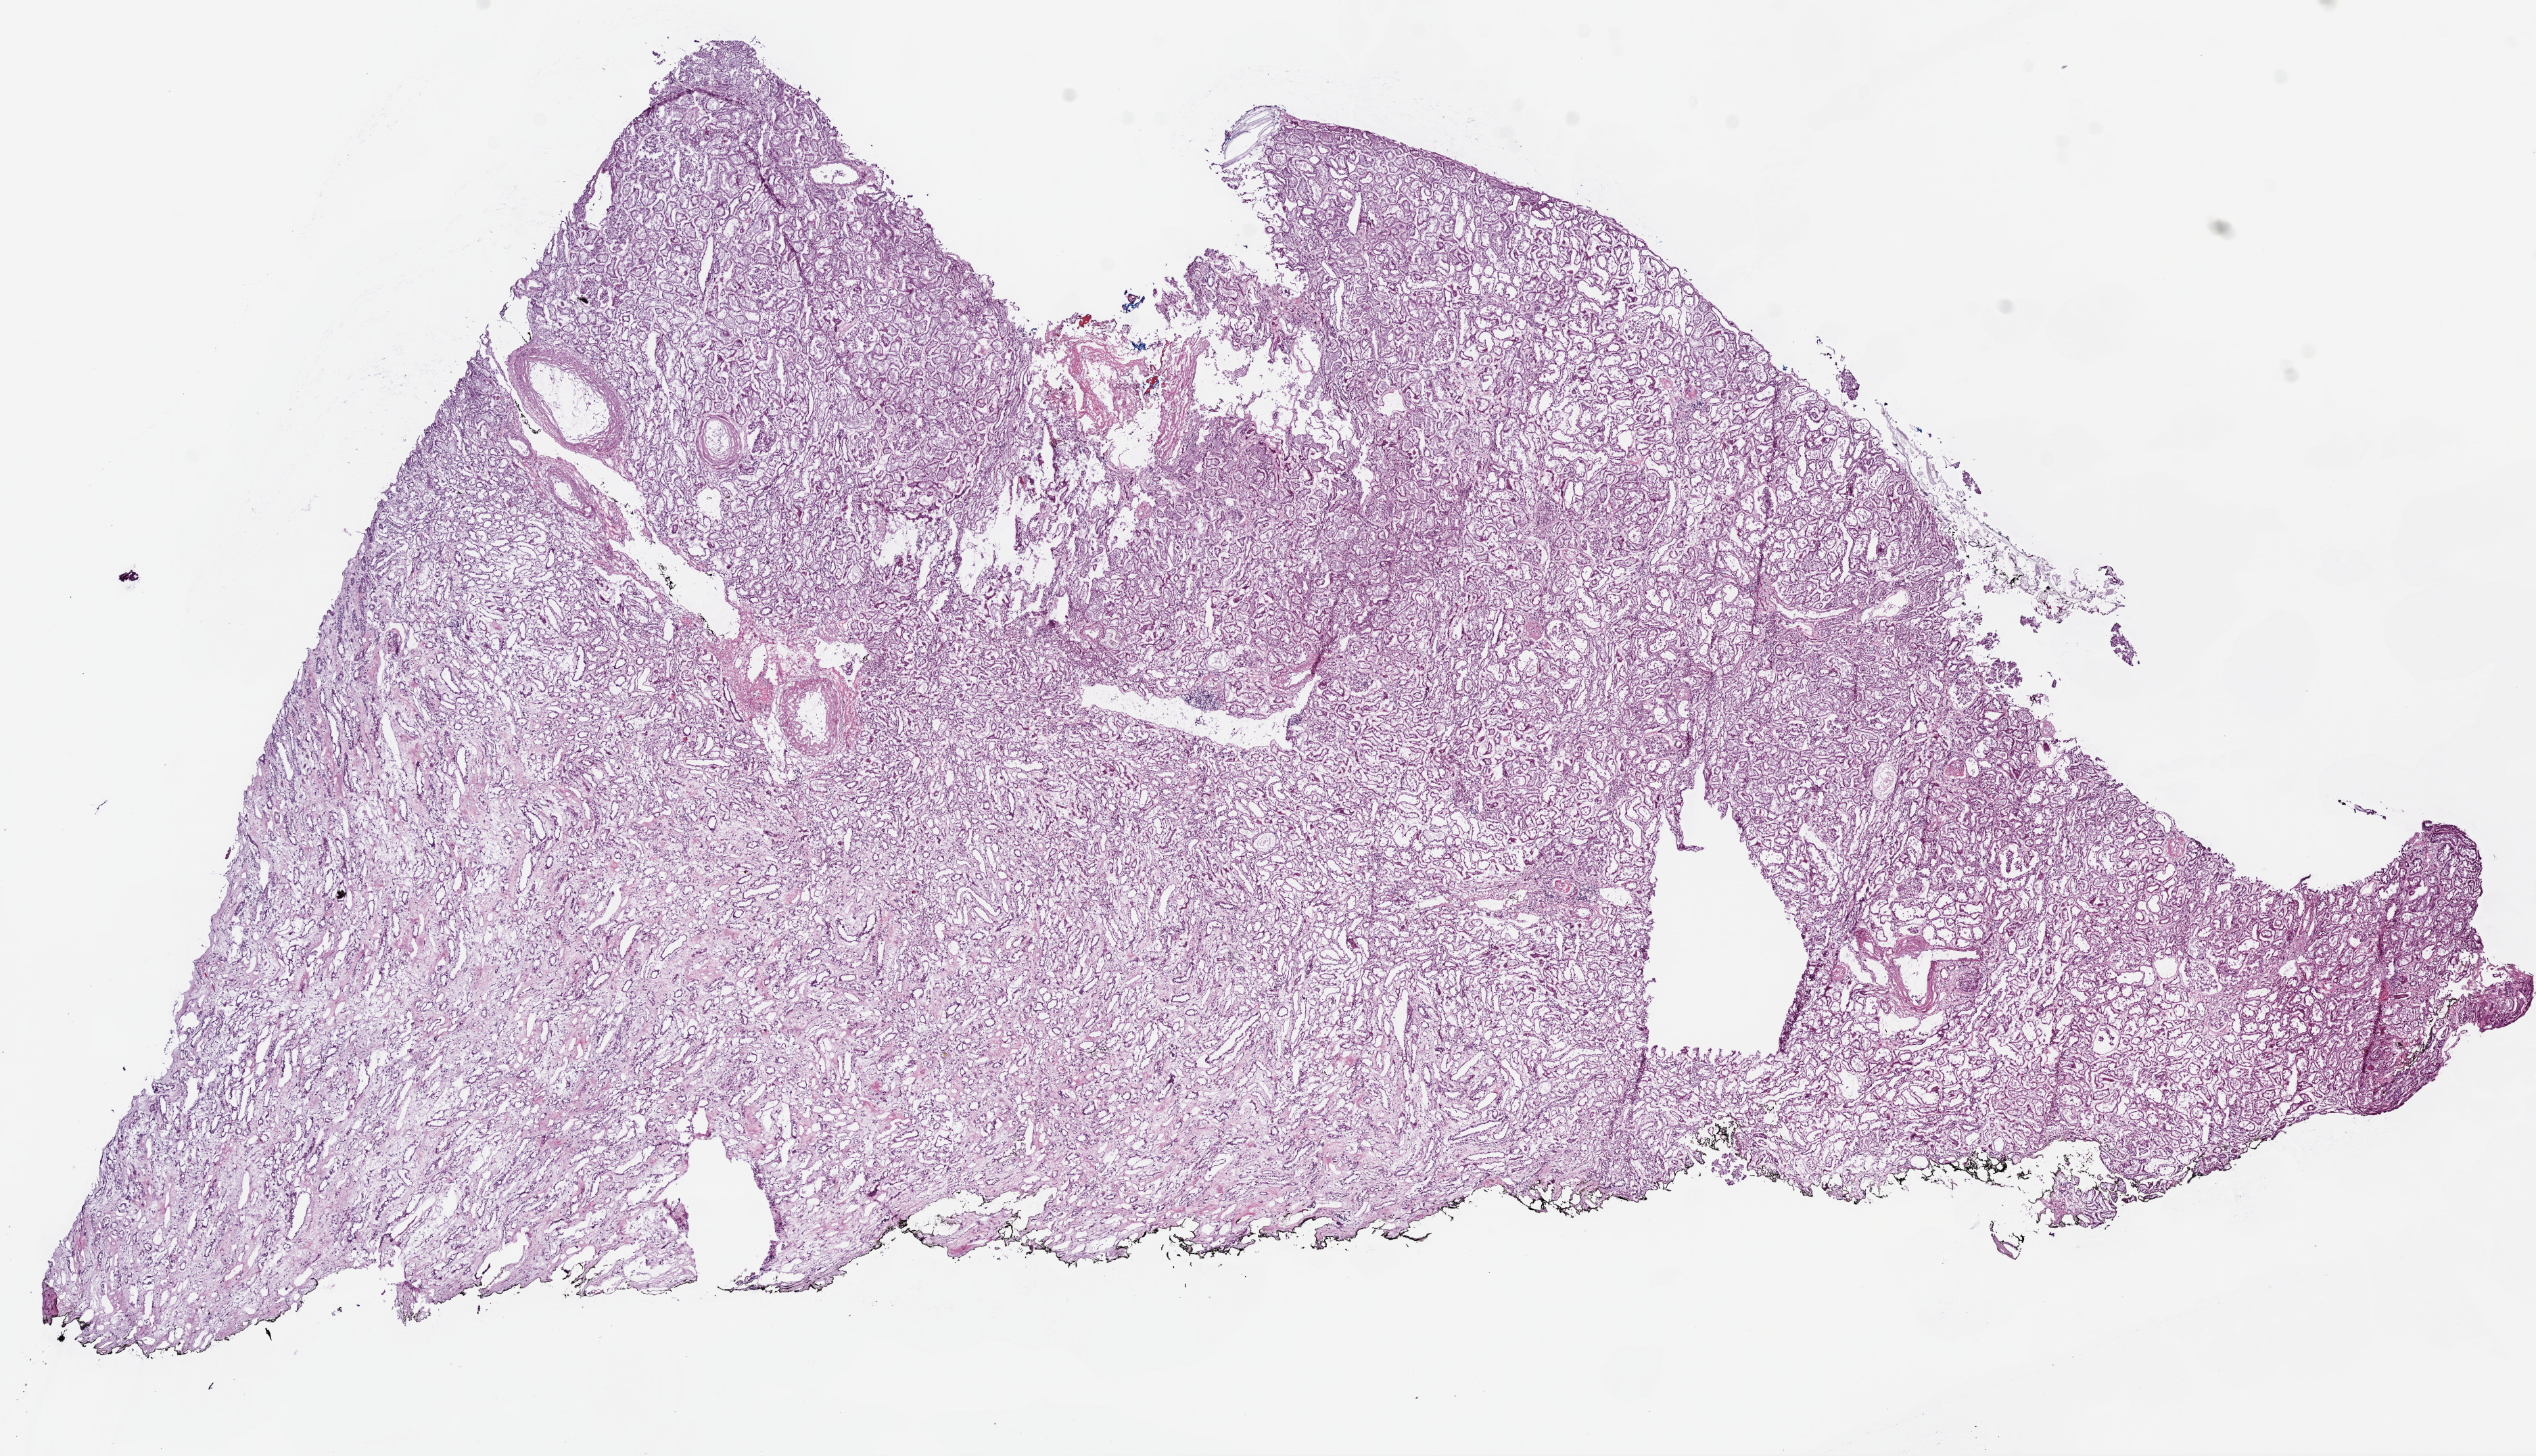
Hematoxylin and eosin (H&E) stained whole-slide image, whole scanned area (about 15.0 x 8.6 mm, acquisition: 20x scan) shown as a low-resolution overview; frozen section from the bottom of the tissue portion; solid tissue normal (non-tumour tissue) sample from the kidney. Female, age 75 years at initial diagnosis.
This section: solid tissue normal sample (biorepository sample class). Patient diagnosis: Clear cell adenocarcinoma, NOS.